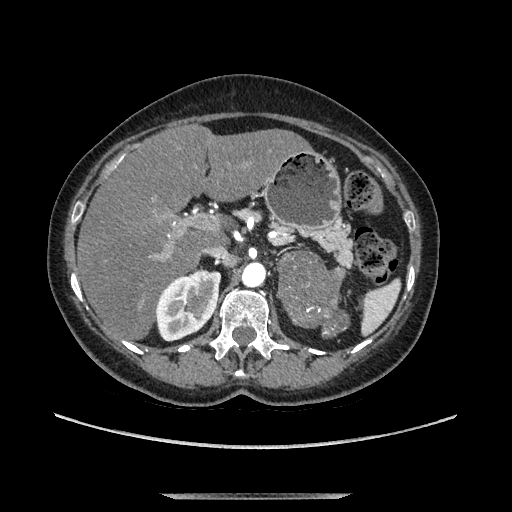
Contrast-enhanced abdominal CT, one axial slice. Position 75 of 169 along the scan axis. Soft-tissue window (W 400 / L 40 HU). 512 × 512 image matrix, field of view 400 × 400 mm. Female patient. From the clinical record (not read from this slice): diagnosis: adrenocortical carcinoma; tumour side: left adrenal.
Annotated regions visible in this slice (semi-automatic segmentation, software-assisted and operator-edited):
- mass: bounding box (x1, y1, x2, y2) in pixels: (278, 254, 347, 339)